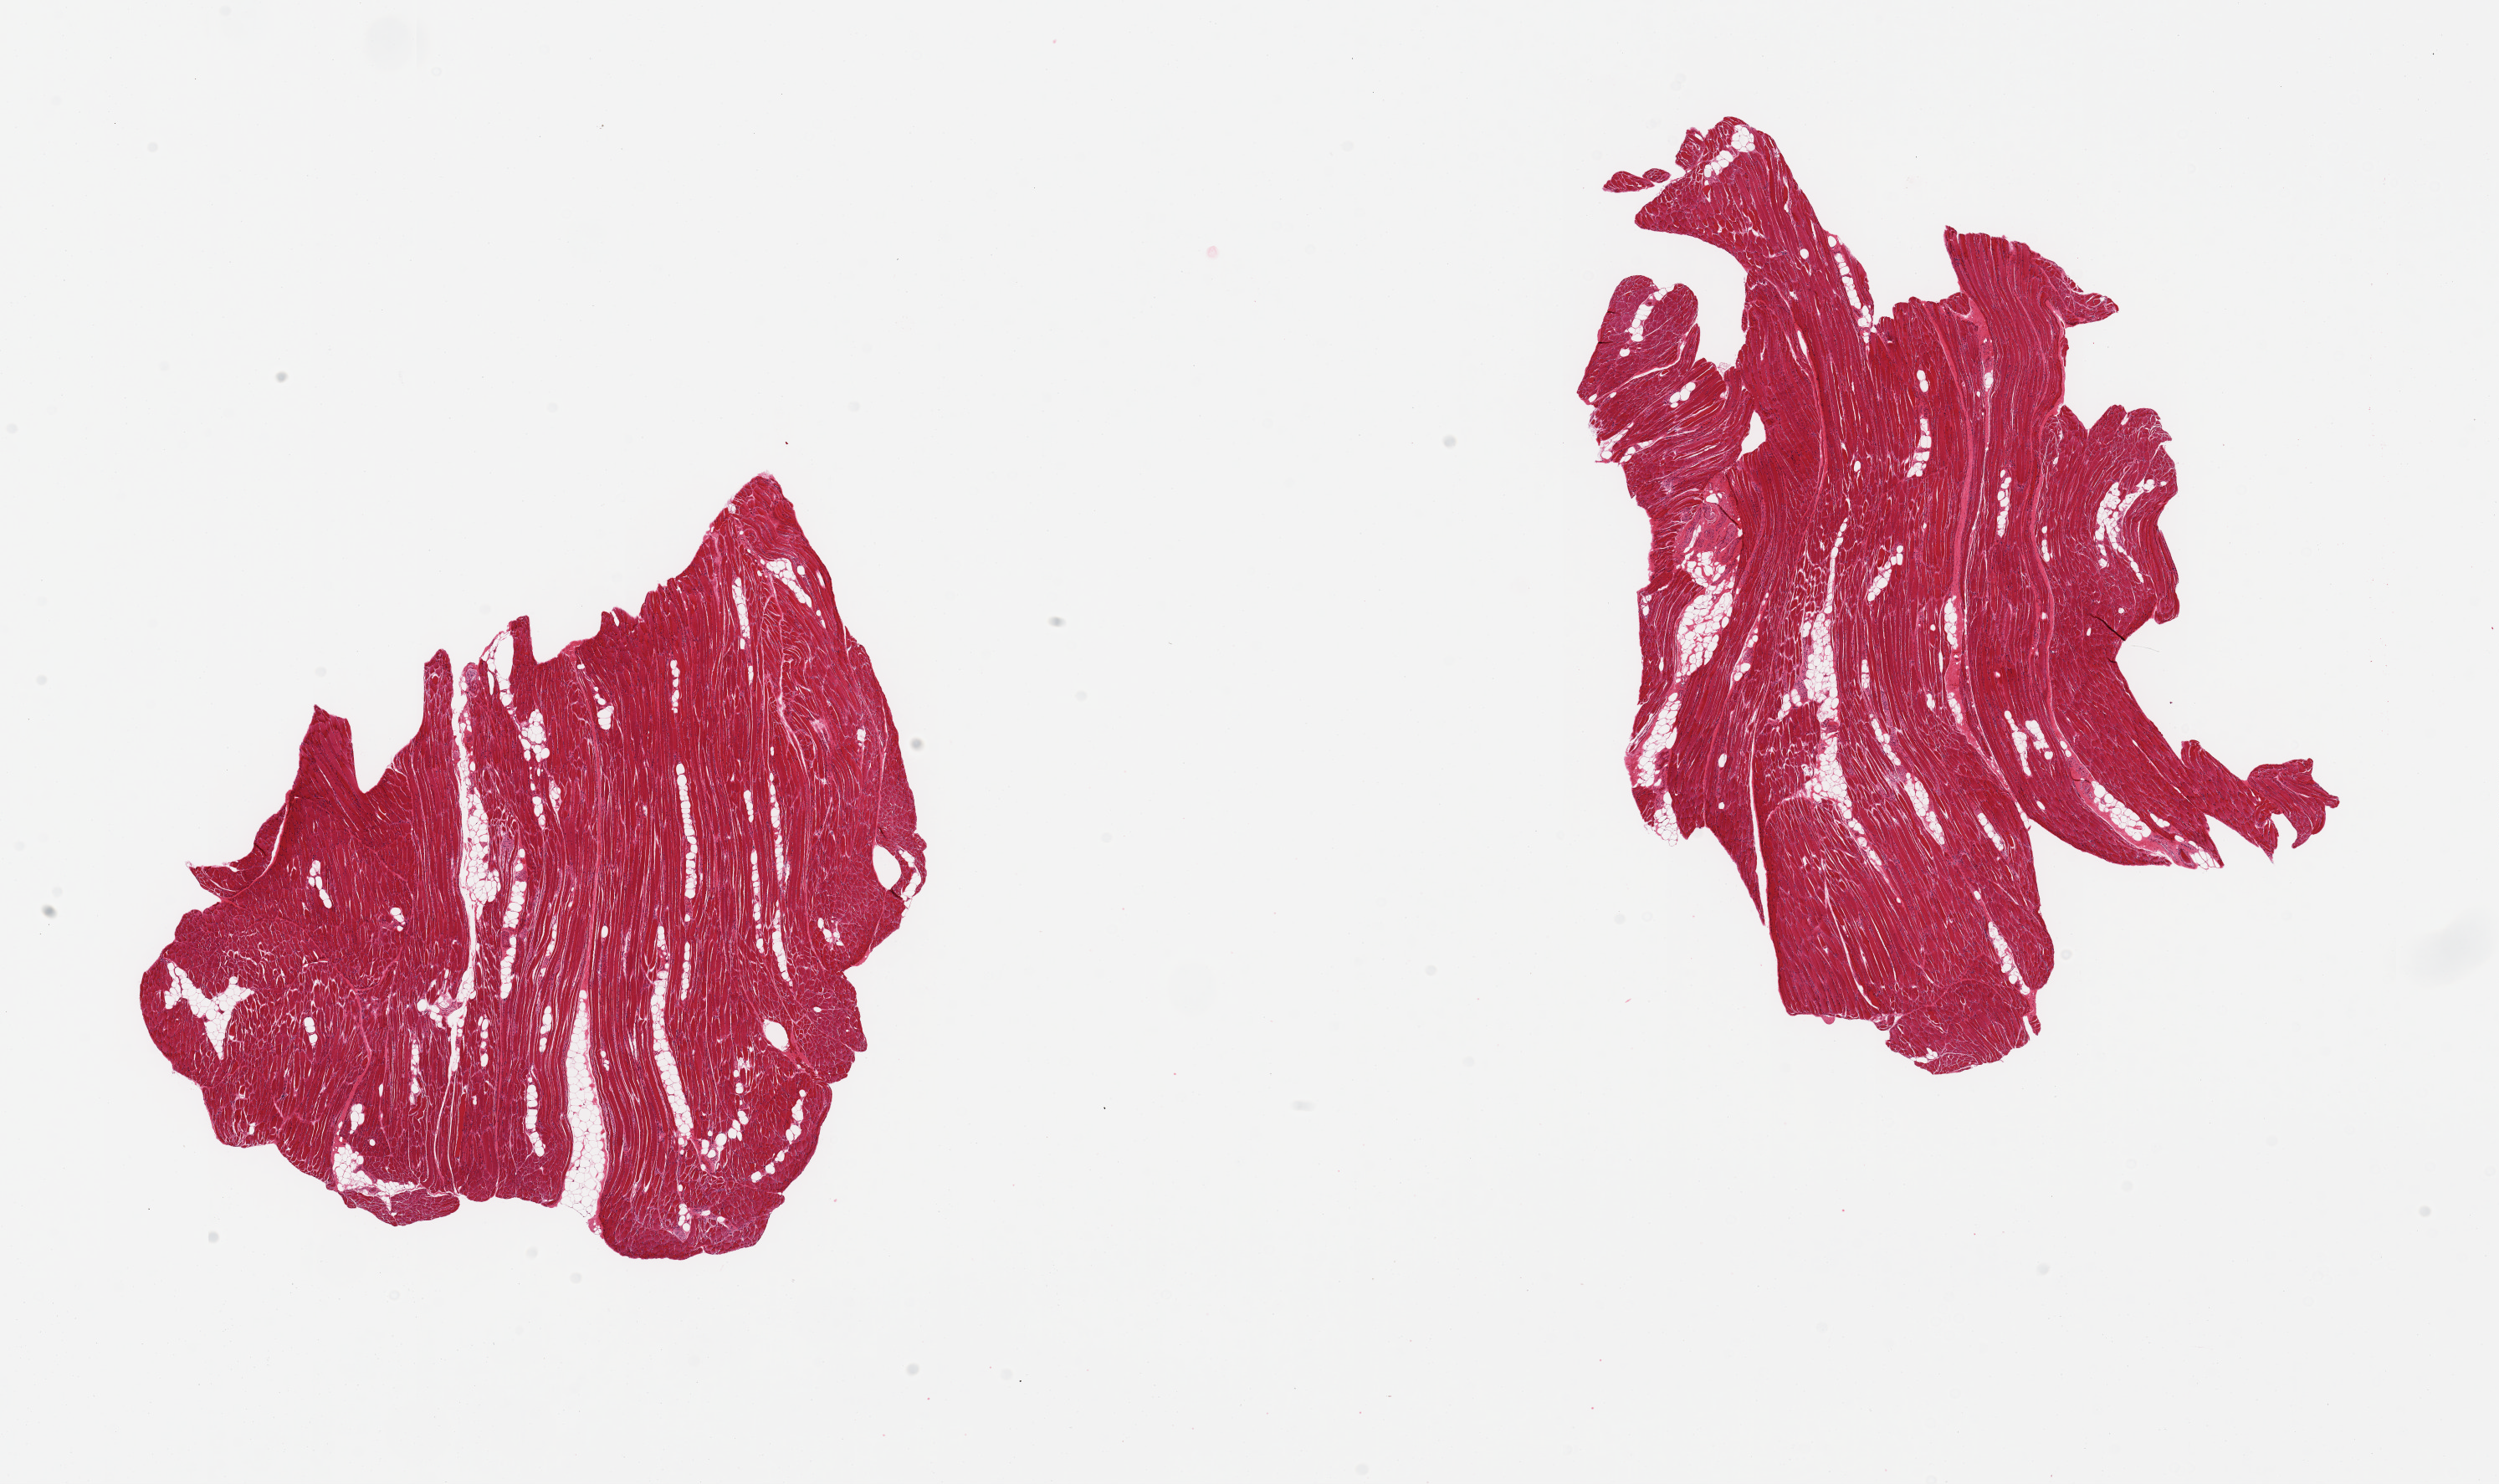
H&E whole-slide image — a low-resolution overview of the entire scanned area, about 23.6 x 14.0 mm. PAXgene-fixed paraffin-embedded (PFPE) section. Sampled site (target tissue): skeletal muscle. Donor tissue sample. Female donor.
• reviewer comment on this tissue sample: 2 pieces; 5% internal fat content